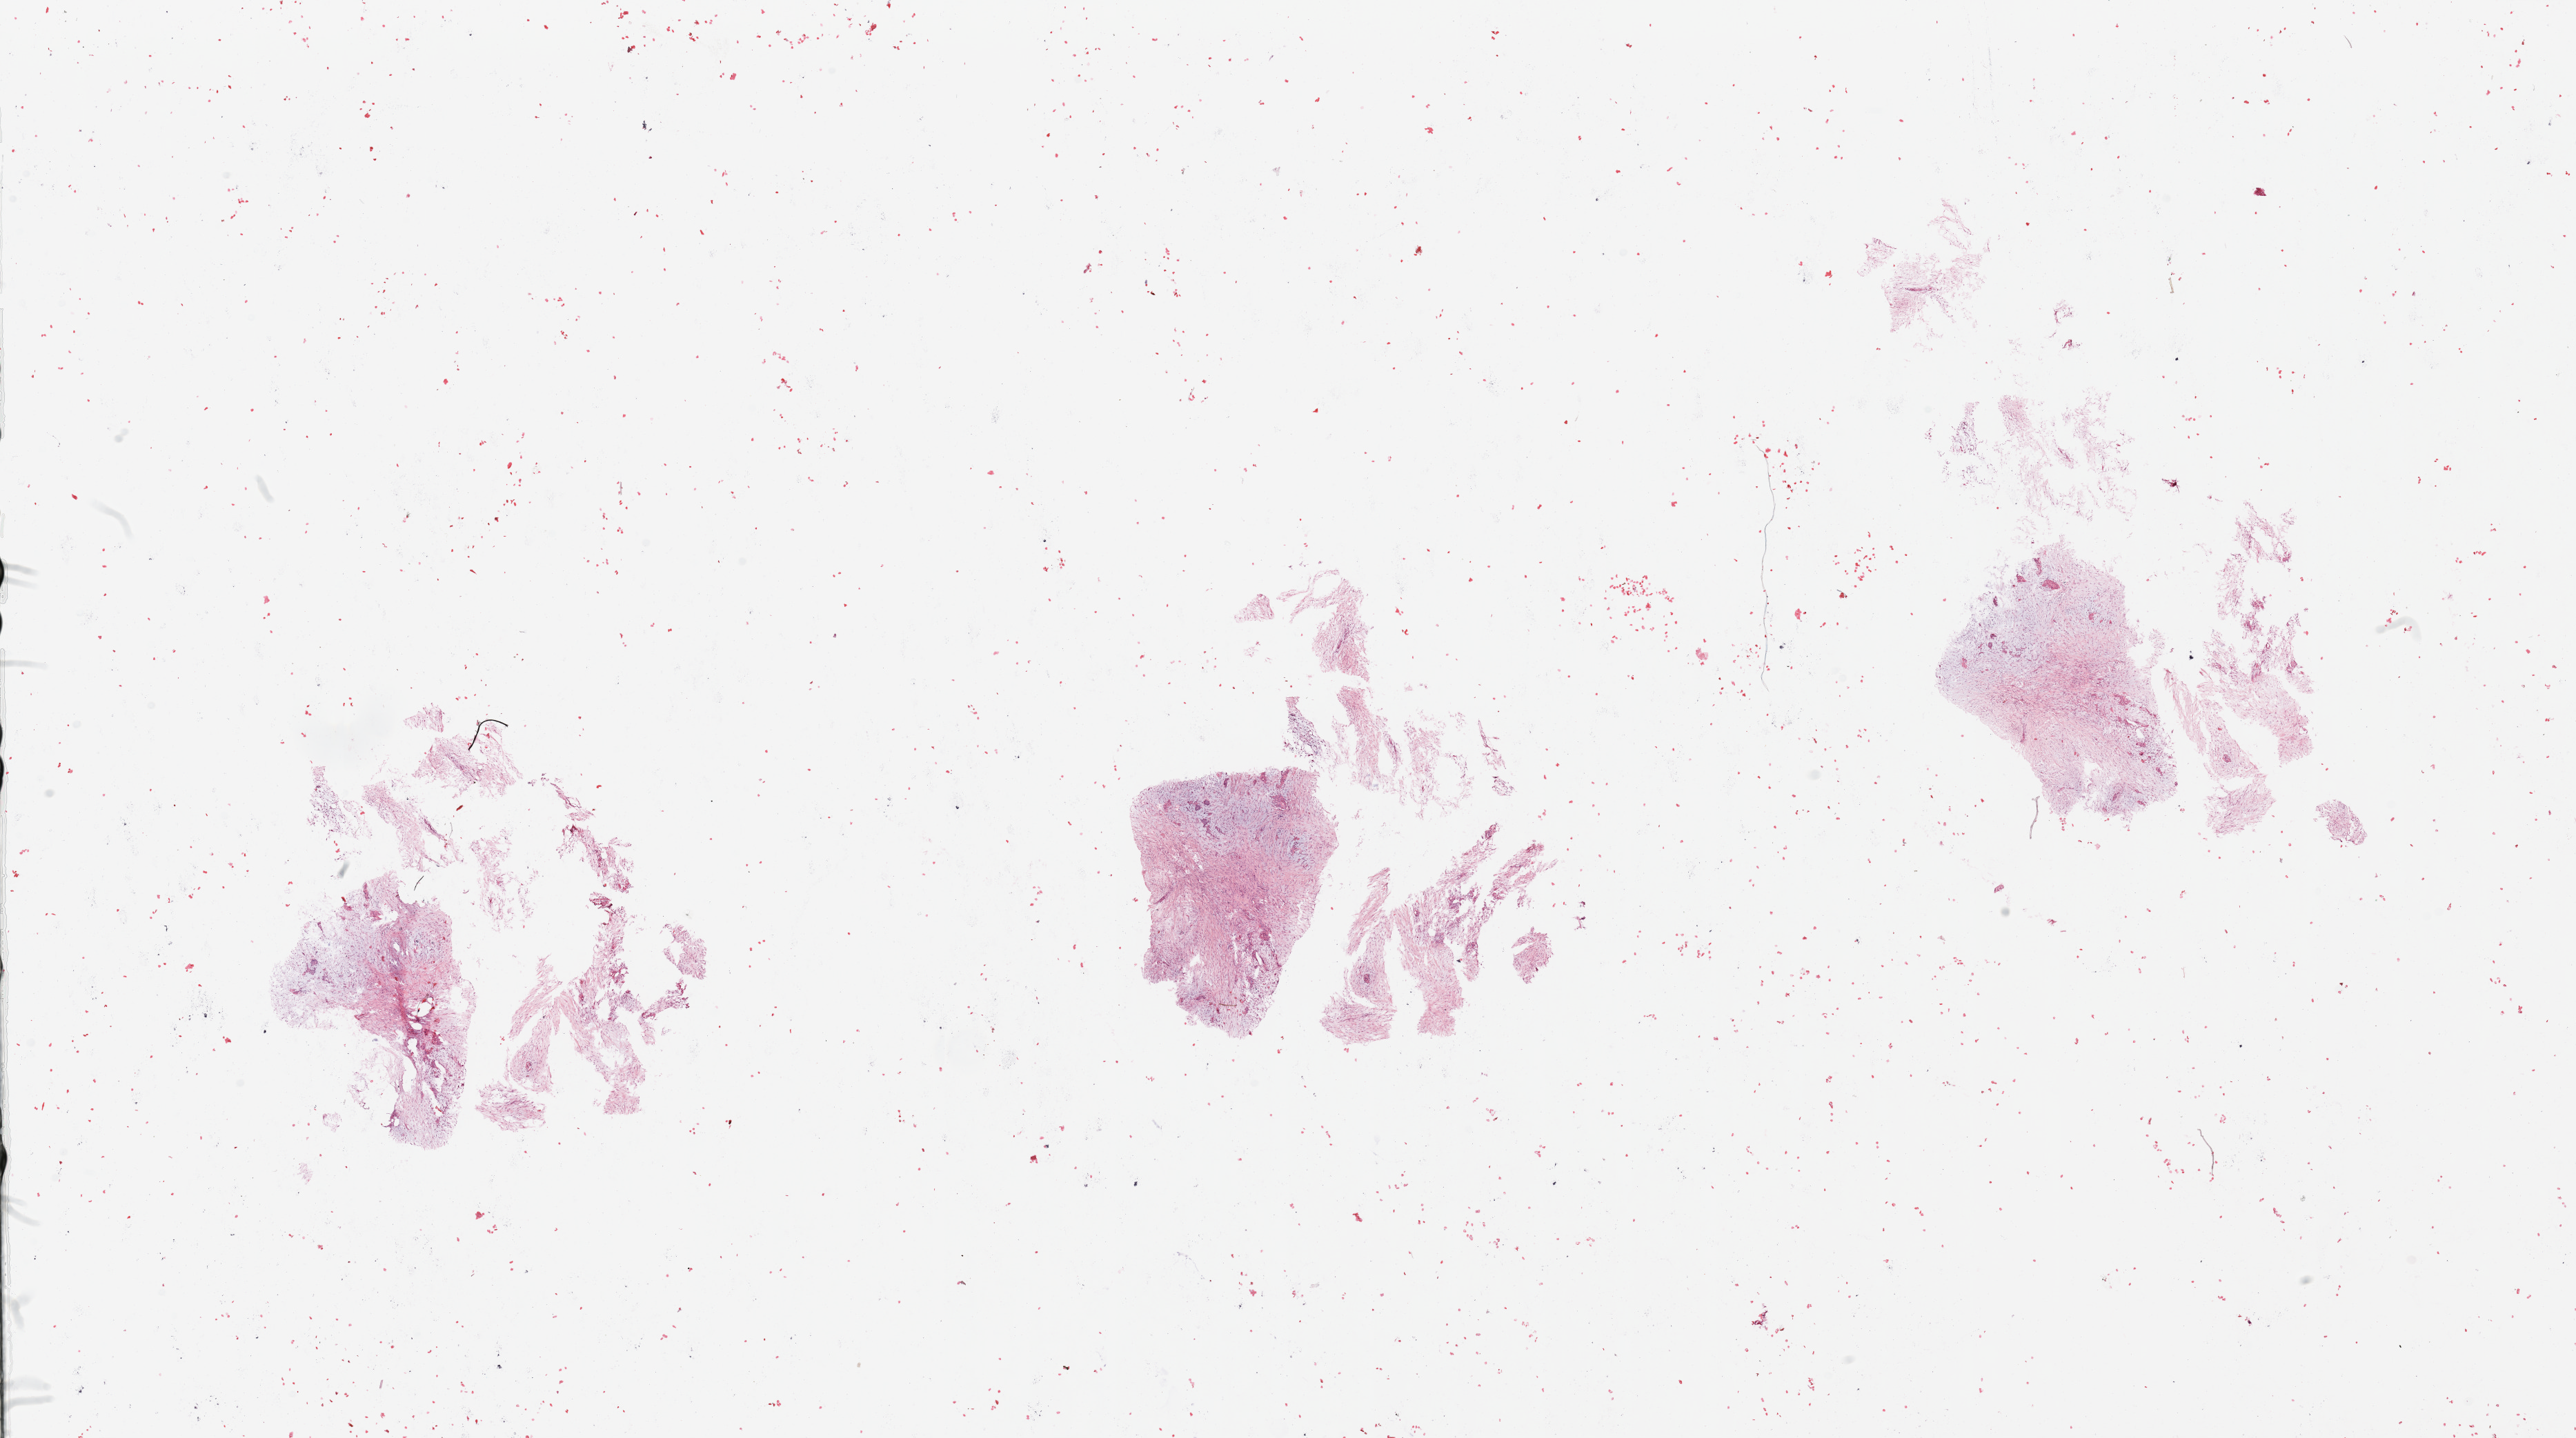
Whole-slide histology image, Hematoxylin and eosin (H&E) stained, shown as a low-resolution overview of the whole scanned area (about 29.5 x 16.5 mm, from a 20x scan), tumour tissue sample, pancreas. Male, 53 y/o.
Patient diagnosis (cohort enrolment): ductal adenocarcinoma (pancreas). Primary tumour site (as recorded): head.